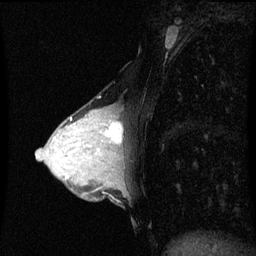
Breast MRI (dynamic contrast-enhanced), one sagittal slice; position 30 of 60 along the scan axis; dynamic contrast-enhanced series, image 2 of 3 at this slice position (ordered by acquisition); 1.5 T; TE 4.2 ms, TR 8.9 ms; 2 mm slice thickness; 256 × 256 image matrix. Patient: female, 33 years. From the clinical record (not read from this slice): setting: breast cancer imaged before/during neoadjuvant chemotherapy; receptor status: HER2-positive.
Outlined on this slice (semi-automatically segmented with operator editing):
- analysis volume of interest (the breast-tissue region the enhancement analysis was run in; not a lesion): bounding box (x1, y1, x2, y2) in pixels: (95, 108, 125, 153)
- tumour enhancement mask (voxels above the 70 % enhancement threshold inside the analysis volume of interest): (105, 122, 123, 143)